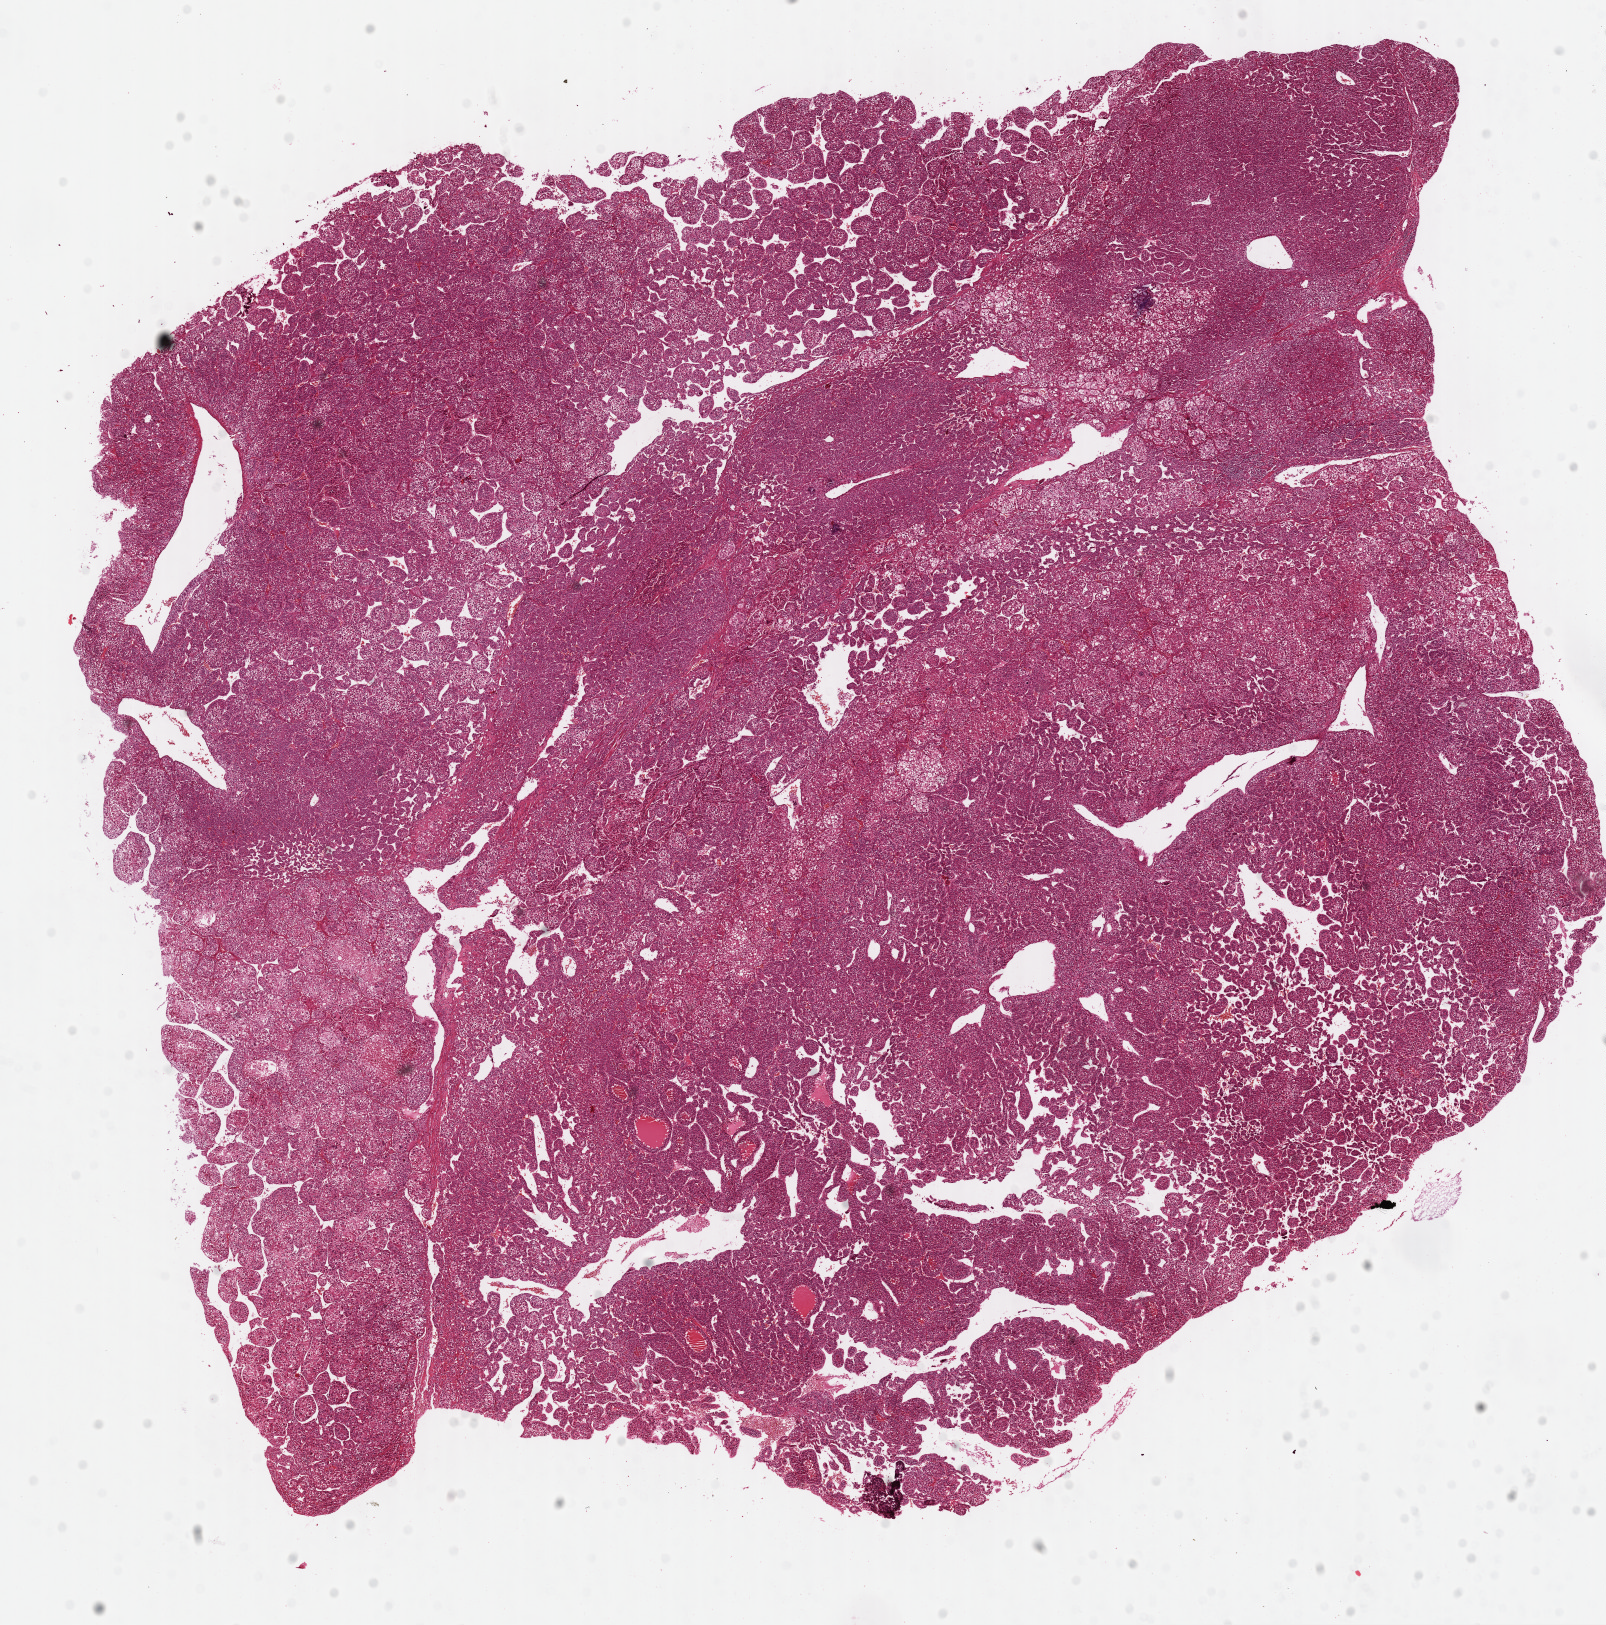
H&E-stained whole-slide image, whole scanned area (about 12.7 x 12.8 mm) shown as a low-resolution overview. Formalin-fixed paraffin-embedded (FFPE) diagnostic section. Primary tumour sample from the liver. Female, age 24 years at initial diagnosis. Histologic grade: G1 (well differentiated).
AJCC pathologic stage: IIIA (6th edition). Diagnosis: Hepatocellular carcinoma, NOS. TNM: T3 N0 M0.